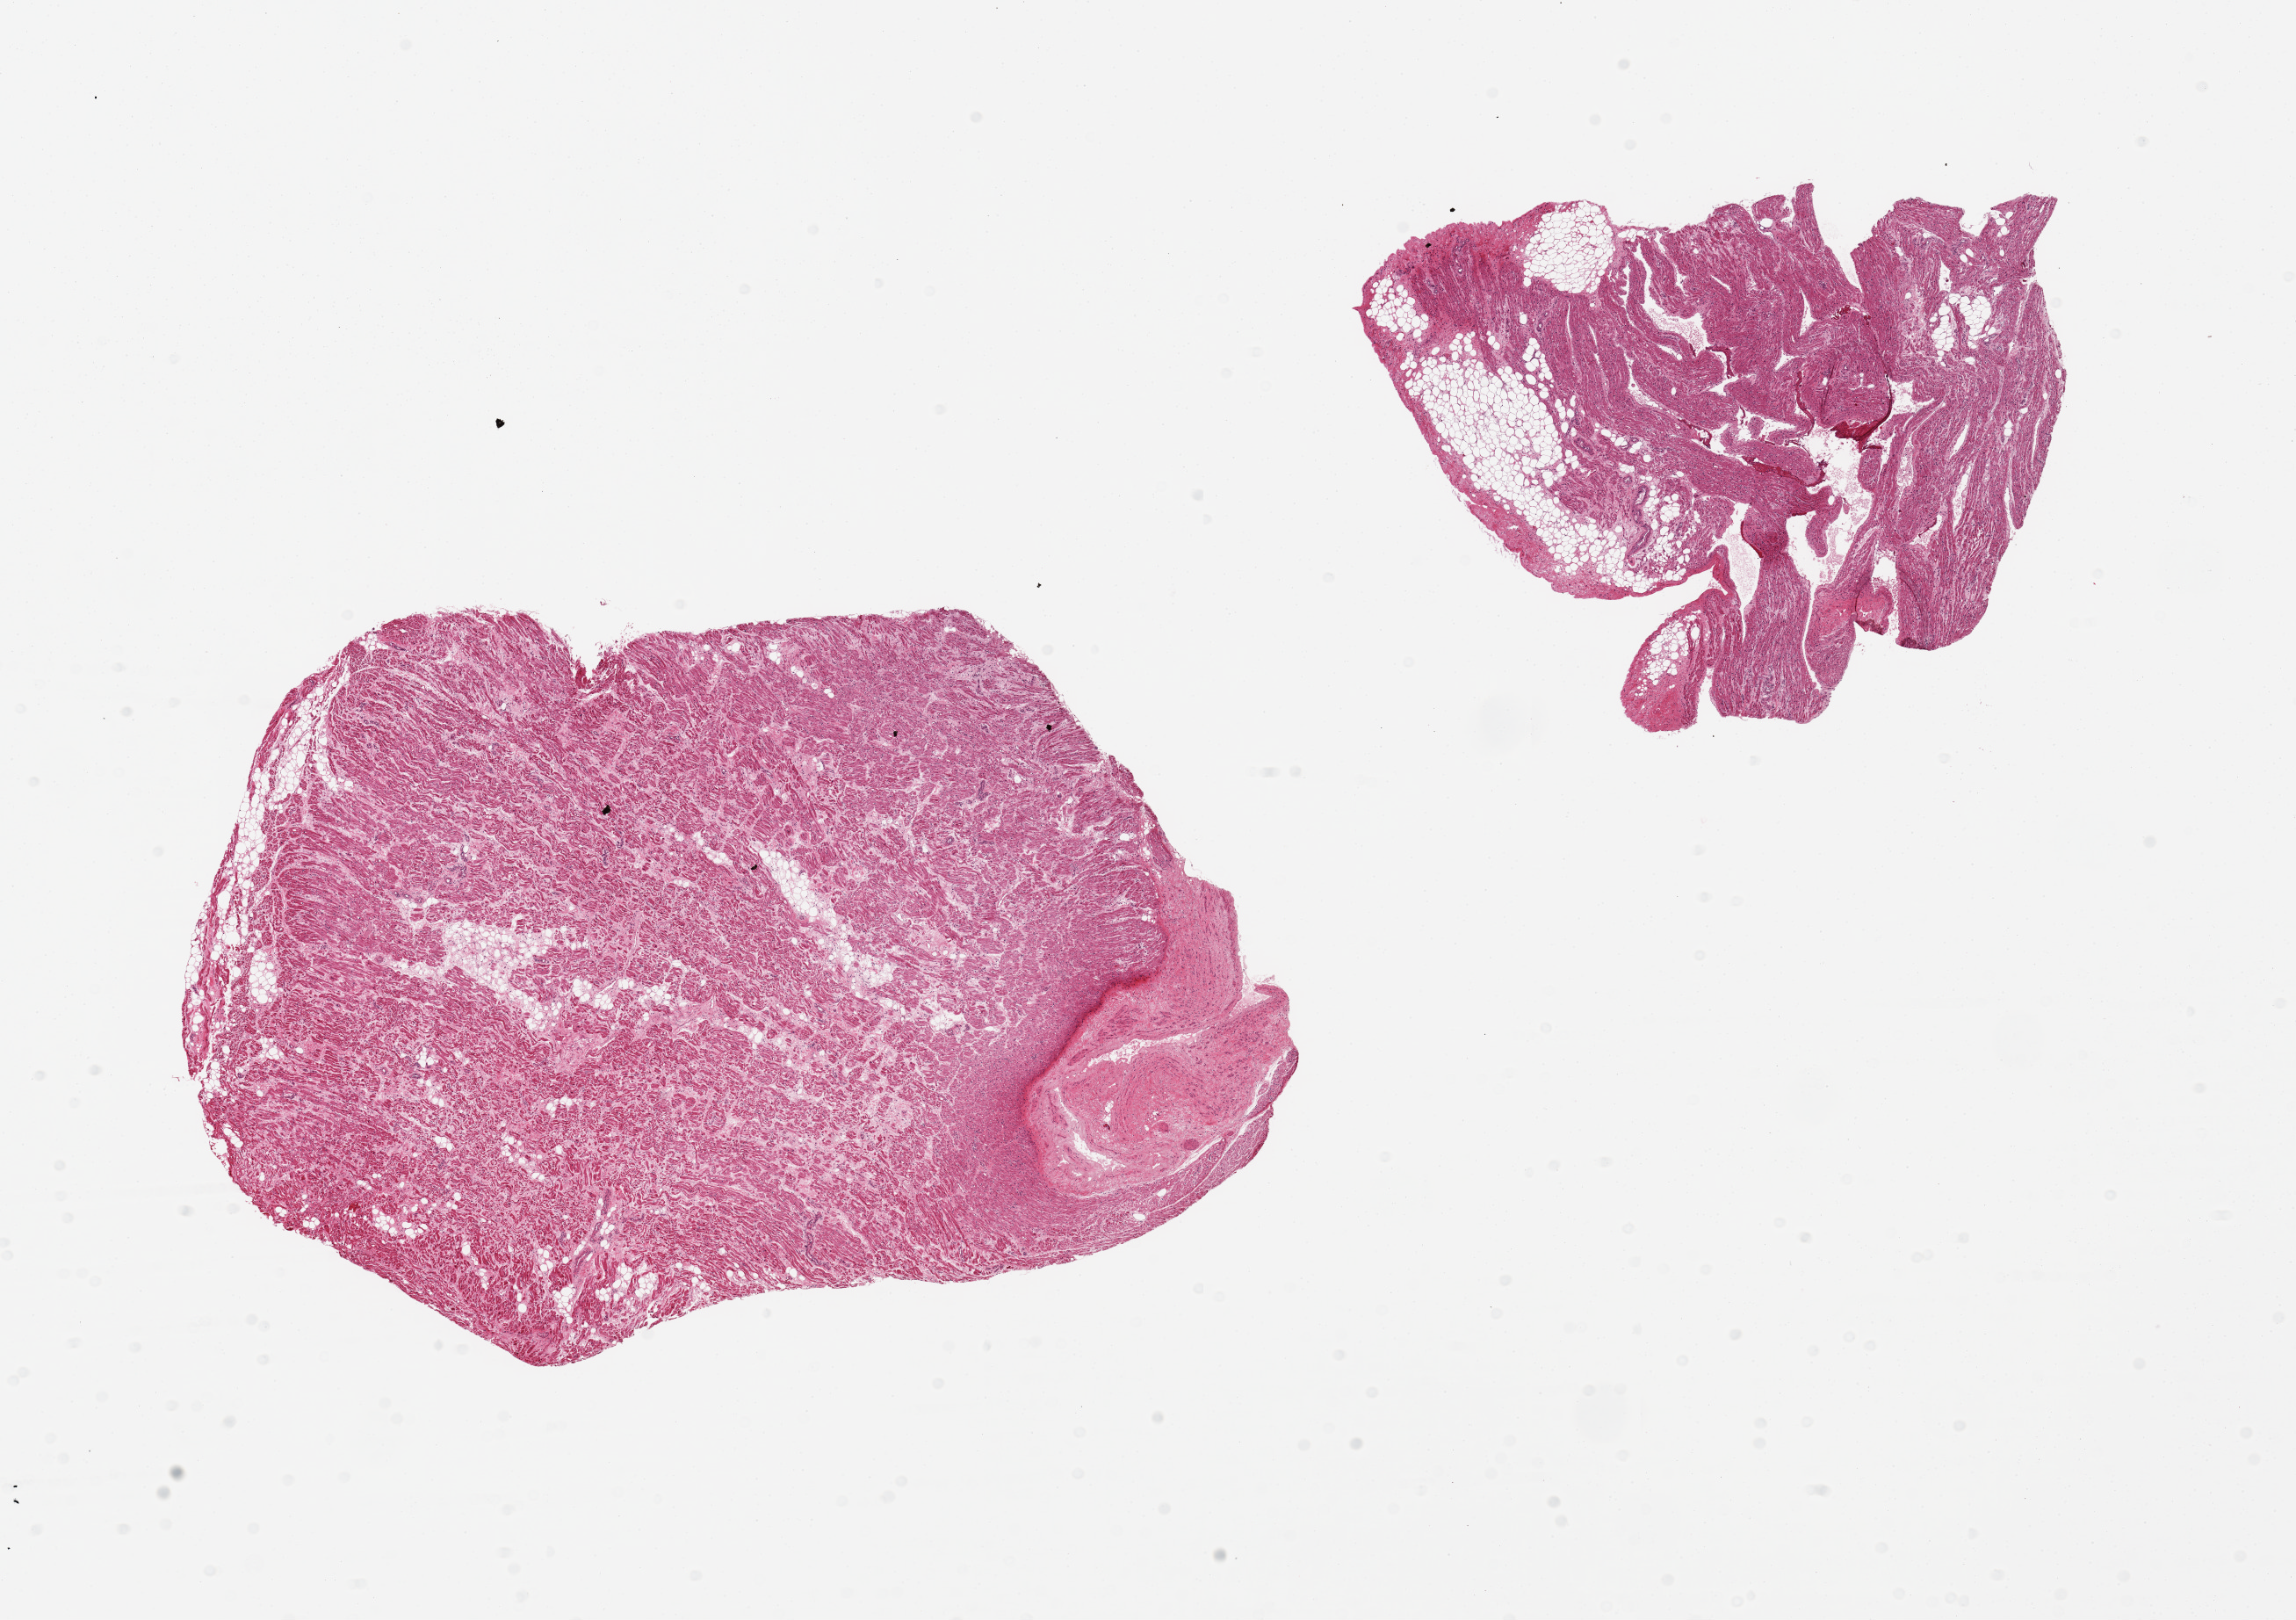
Hematoxylin and eosin (H&E) whole-slide image, brightfield — whole scanned area (about 20.7 x 14.6 mm, from a 20x scan) shown as a low-resolution overview; PAXgene-fixed, paraffin-embedded tissue; section of auricular appendage (target tissue); tissue donor sample. Female donor.
Review note (as recorded): 2 pieces, 10x7 & 6x5mm.